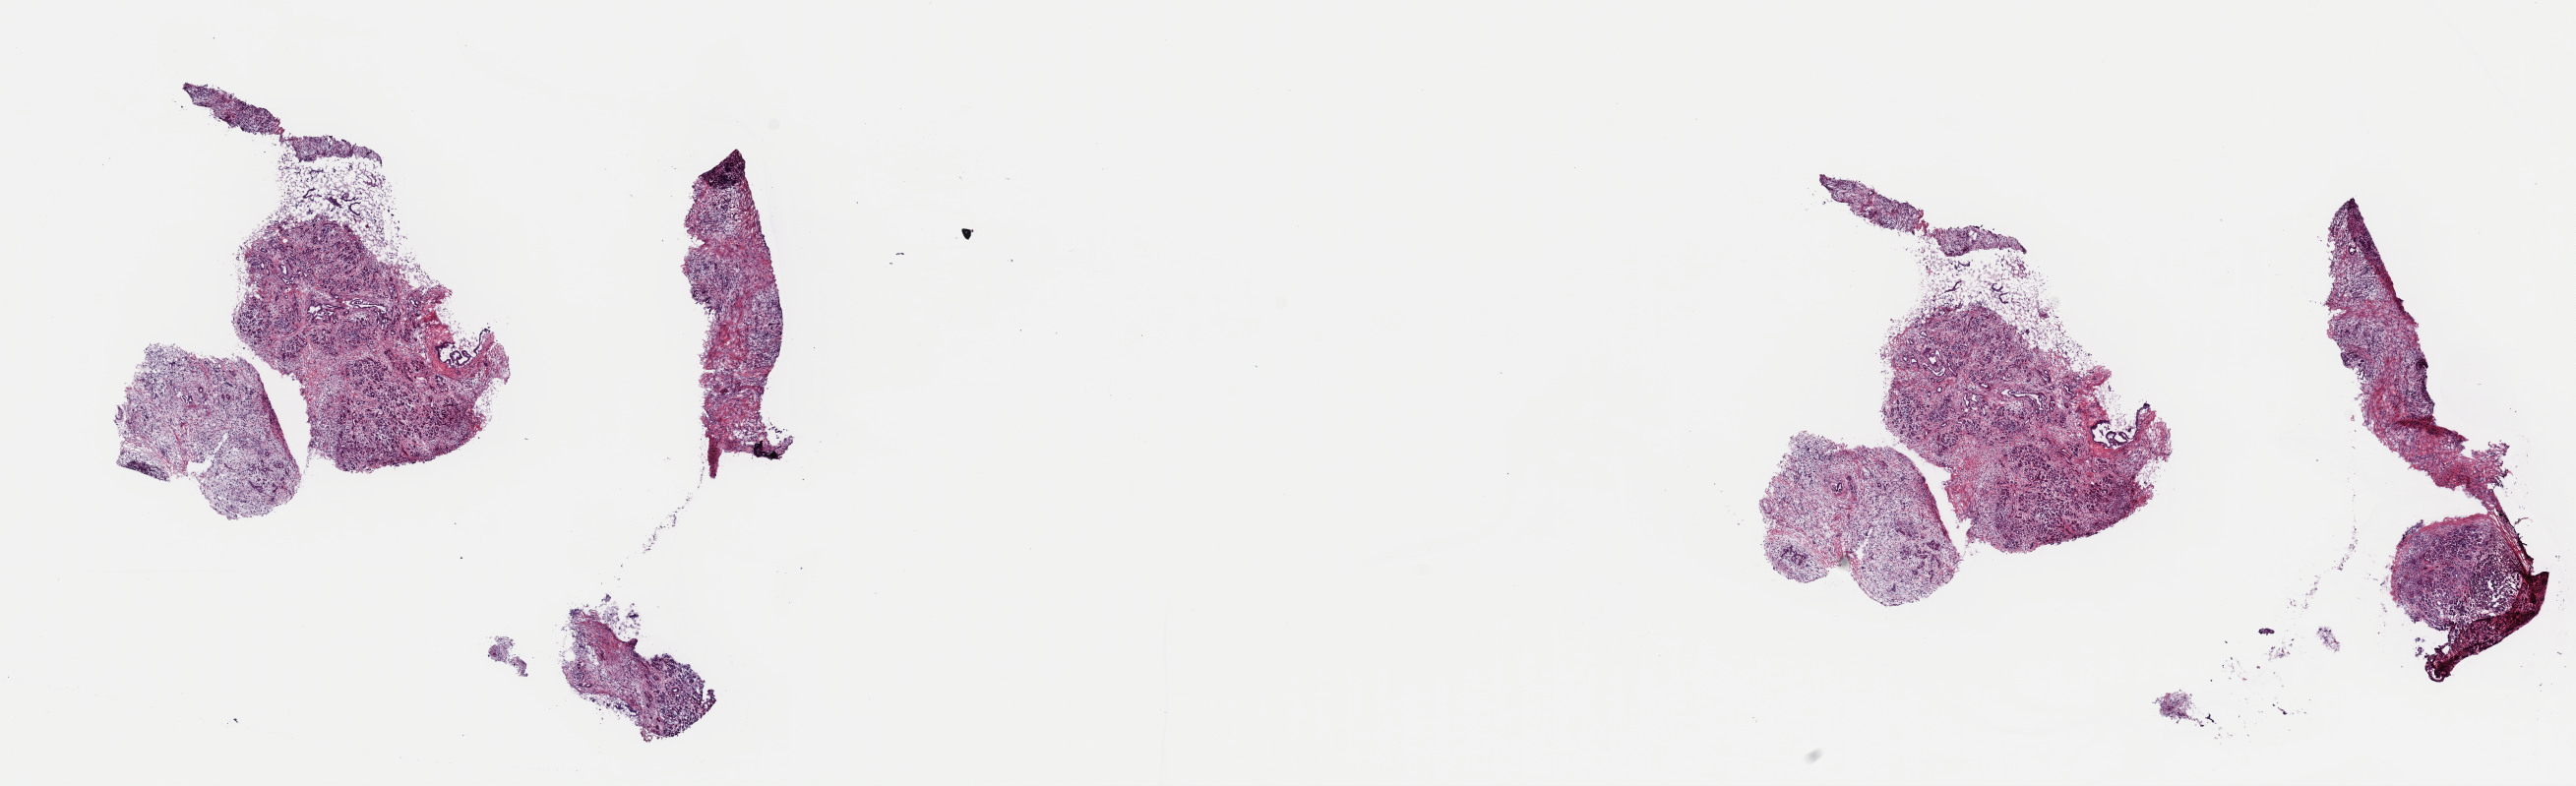
H&E-stained whole-slide image, a low-resolution overview of the entire scanned area, about 20.7 x 6.3 mm (from a 40x scan). Frozen section from the top of the tissue portion. Primary tumour sample from the pancreas. Male patient; age at initial diagnosis 53 years. Histologic grade: G2 (moderately differentiated). Pathologist review of this section (percent, as recorded): tumour cells 20%, tumour nuclei 65%, normal cells 3%, stromal cells 74%, necrosis 3%. Infiltration values recorded for this section: lymphocyte infiltration 10%, monocyte infiltration 2%, neutrophil infiltration 2%.
Pathologic diagnosis: Adenocarcinoma, NOS (head of pancreas). TNM: T3 N0 MX. Lymph nodes positive (case pathology): 0 of 21 examined. AJCC pathologic stage: IIA (7th edition).